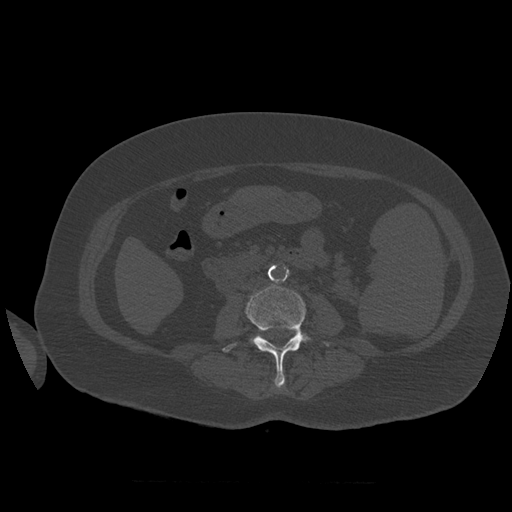
CT including the spine, one axial slice. Slice 228 of 399 in the series (ordered by position). Reconstruction kernel STANDARD. 120 kVp. Bone window (W 1800 / L 400 HU). 512 × 512 image matrix, field of view 404 × 404 mm. Patient age 81 years. Case-level facts recorded for this patient, not image findings: primary cancer: renal.
Structures marked on this image (semi-automatic segmentation, software-assisted and operator-edited):
- L3 vertebra: box from (x=223, y=286) to (x=329, y=388) px